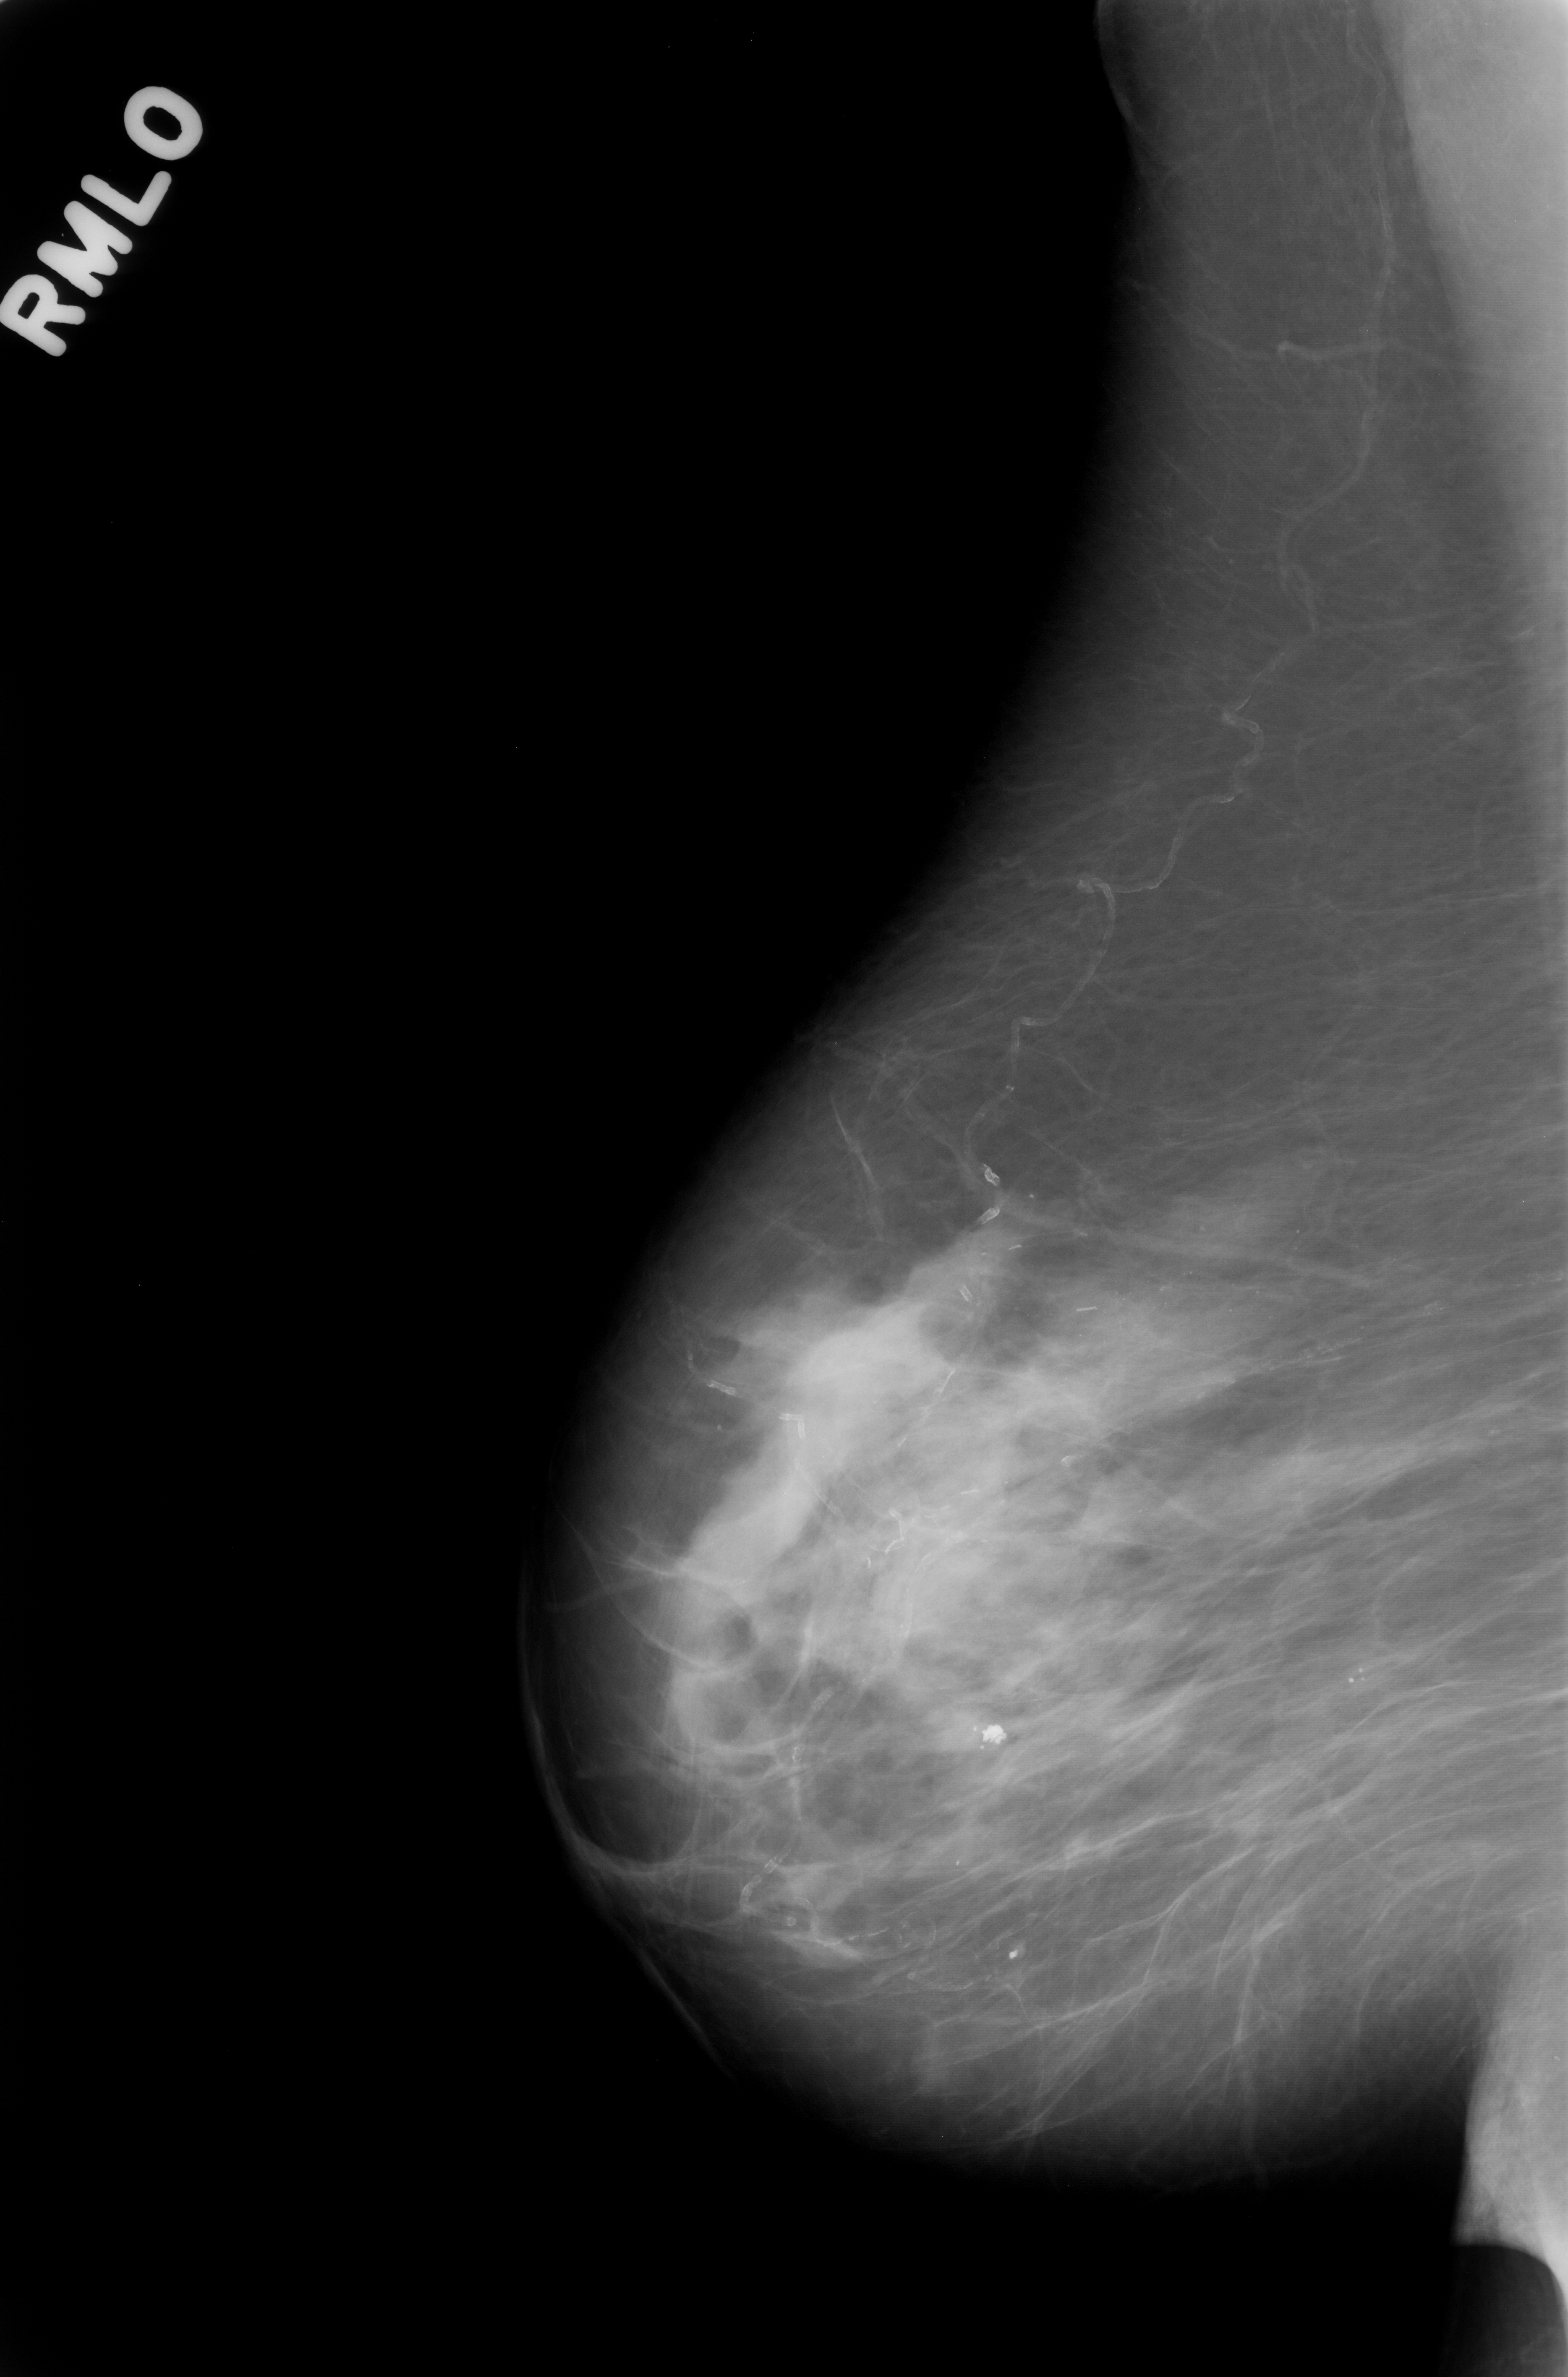
Mammogram (digitized film); right breast; mediolateral oblique (MLO) view; breast composition: scattered fibroglandular densities (BI-RADS density category 2 of 4).
Radiologist-marked abnormalities on this image: calcifications, morphology punctate, distribution segmental; BI-RADS assessment category 4; subtlety rating 2 on a 1 (subtle) to 5 (obvious) scale; pathology result (as recorded, not read from the image): benign.